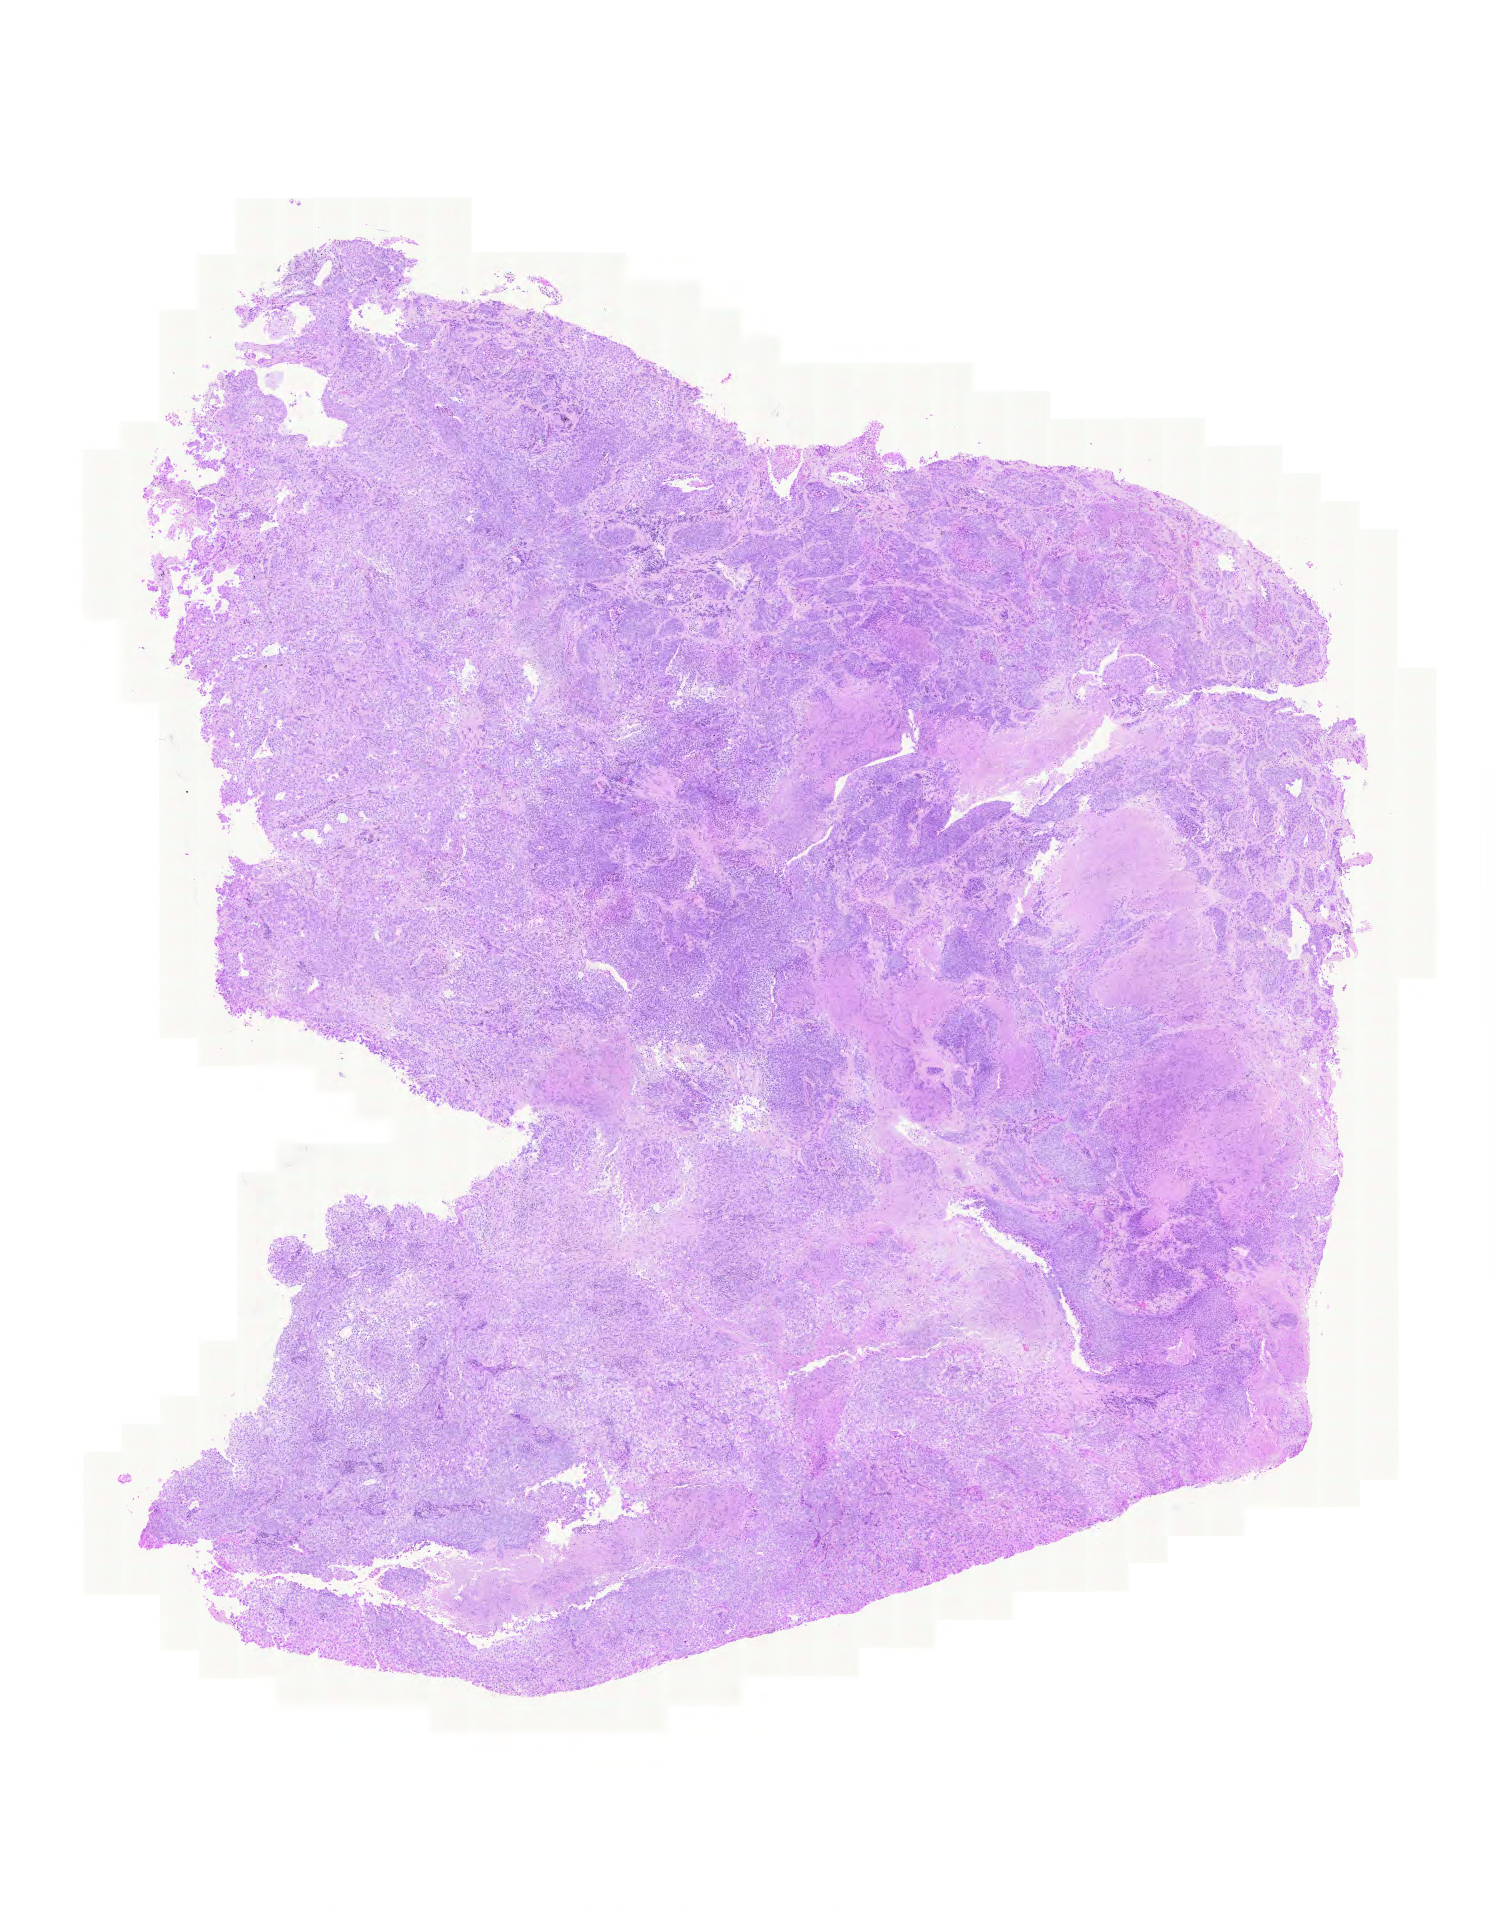
Digitized H&E tissue section (whole slide), low-resolution overview of the scanned area, about 11.1 x 14.2 mm, formalin-fixed paraffin-embedded (FFPE) diagnostic section, sample: primary tumour, lung. Female, age 67 years at initial diagnosis.
AJCC pathologic stage: IV. Diagnosis: Adenocarcinoma with mixed subtypes (lower lobe, lung).